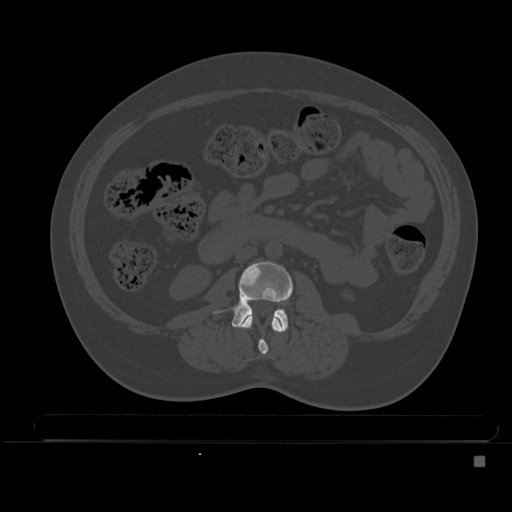
CT including the spine, one axial slice. Position 159 of 495 along the scan axis. Bone window (W 1800 / L 400 HU). 512 × 512 image matrix, field of view 404 × 404 mm. Female patient, age 33 years. Case-level facts recorded for this patient, not image findings: primary cancer: breast; vertebrae with lytic lesions (as recorded): T1.
Annotated regions visible in this slice (semi-automatic segmentation, software-assisted and operator-edited):
- L2 vertebra: bounding box <239,315,284,355> (left, top, right, bottom; pixels)
- L3 vertebra: <232,261,293,331>